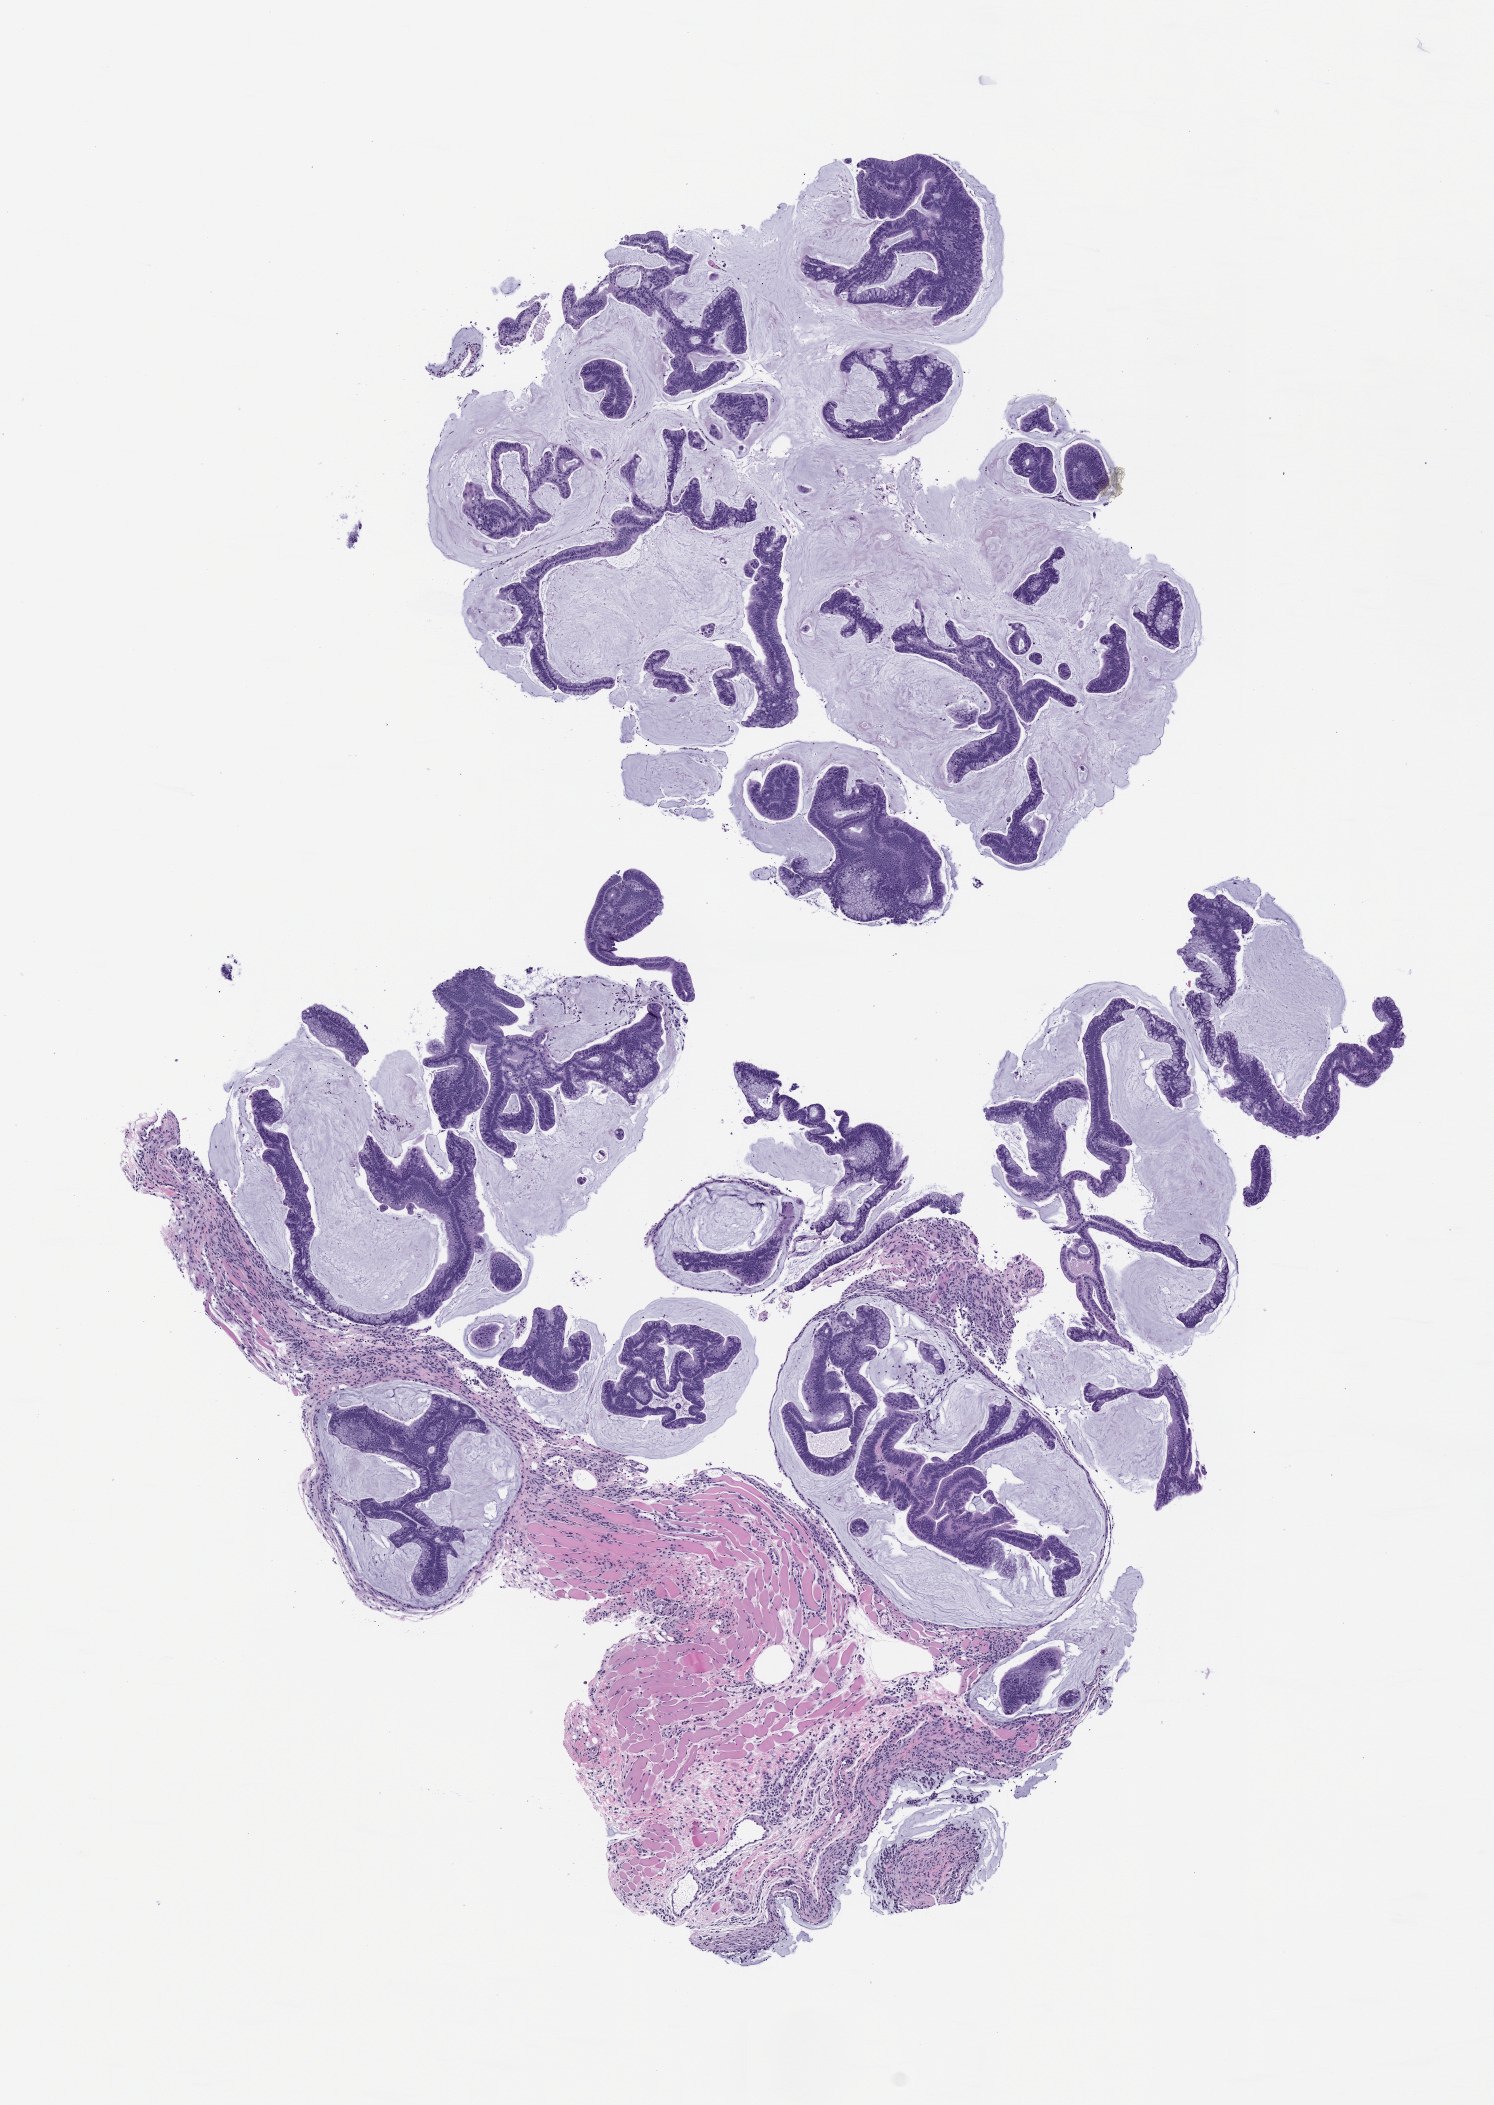
Hematoxylin and eosin (H&E) whole-slide image of a patient-derived xenograft (PDX) tumor grown in a mouse, passage 2, low-resolution overview of the scanned area, about 6.0 x 8.5 mm, formalin-fixed, paraffin-embedded (FFPE) tissue, originating tumor site category: colon.
Originating patient diagnosis: Colon Adenocarcinoma.